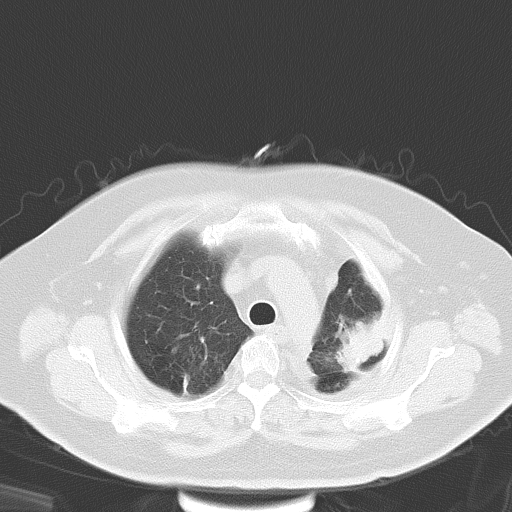
Chest CT, one axial slice; position 23 of 29 along the scan axis; lung window (W 1500 / L -600 HU); 512 × 512 image matrix. Female patient, age 69 years. Case-level facts recorded for this patient, not image findings: clinical TNM (as recorded): T3 N0 M0.
Outlined on this slice (rectangle marked by the reading radiologist):
- lung tumour (recorded histology: adenocarcinoma): bounding box (x1, y1, x2, y2) in pixels: (341, 307, 386, 377)